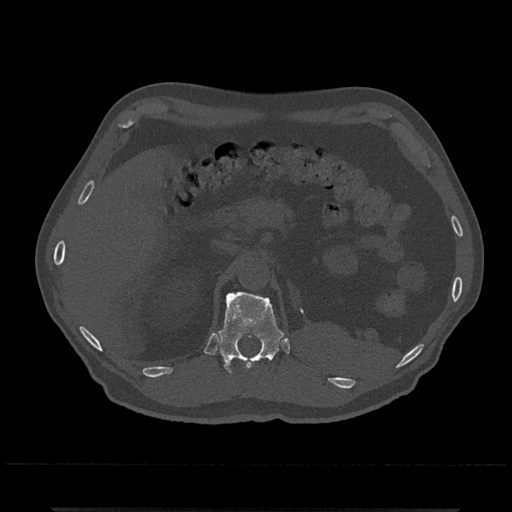
CT including the spine, one axial slice; position 440 of 797 along the scan axis; reconstruction kernel Br40s/3; 120 kVp; bone window (W 1800 / L 400 HU); 0.5 mm slice thickness; 512 × 512 image matrix, field of view 393 × 393 mm. Patient: male, 67 years. Case-level facts recorded for this patient, not image findings: primary cancer: prostate.
Annotated regions visible in this slice (semi-automatically segmented with operator editing):
- T11 vertebra: bounding box <252,361,255,365> (left, top, right, bottom; pixels)
- T12 vertebra: <218,291,284,373>